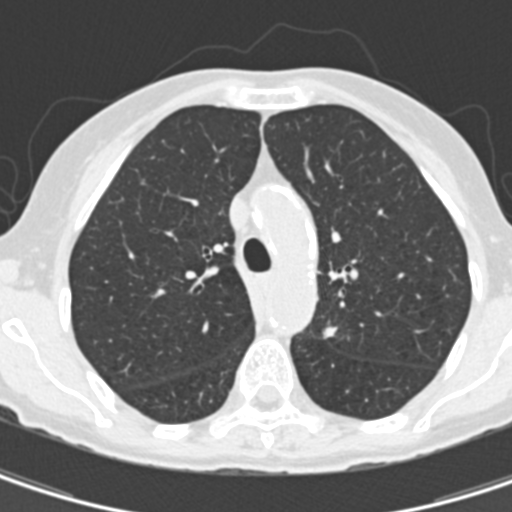
Low-dose screening chest CT, one axial slice; 120 kVp; lung window (W 1500 / L -600 HU); 512 × 512 image matrix, field of view 260 × 260 mm.
Structures marked on this image (expert manual segmentation):
- lesion 1 (tumor, upper lobe of left lung): bounding box (x1, y1, x2, y2) in pixels: (323, 326, 338, 339)